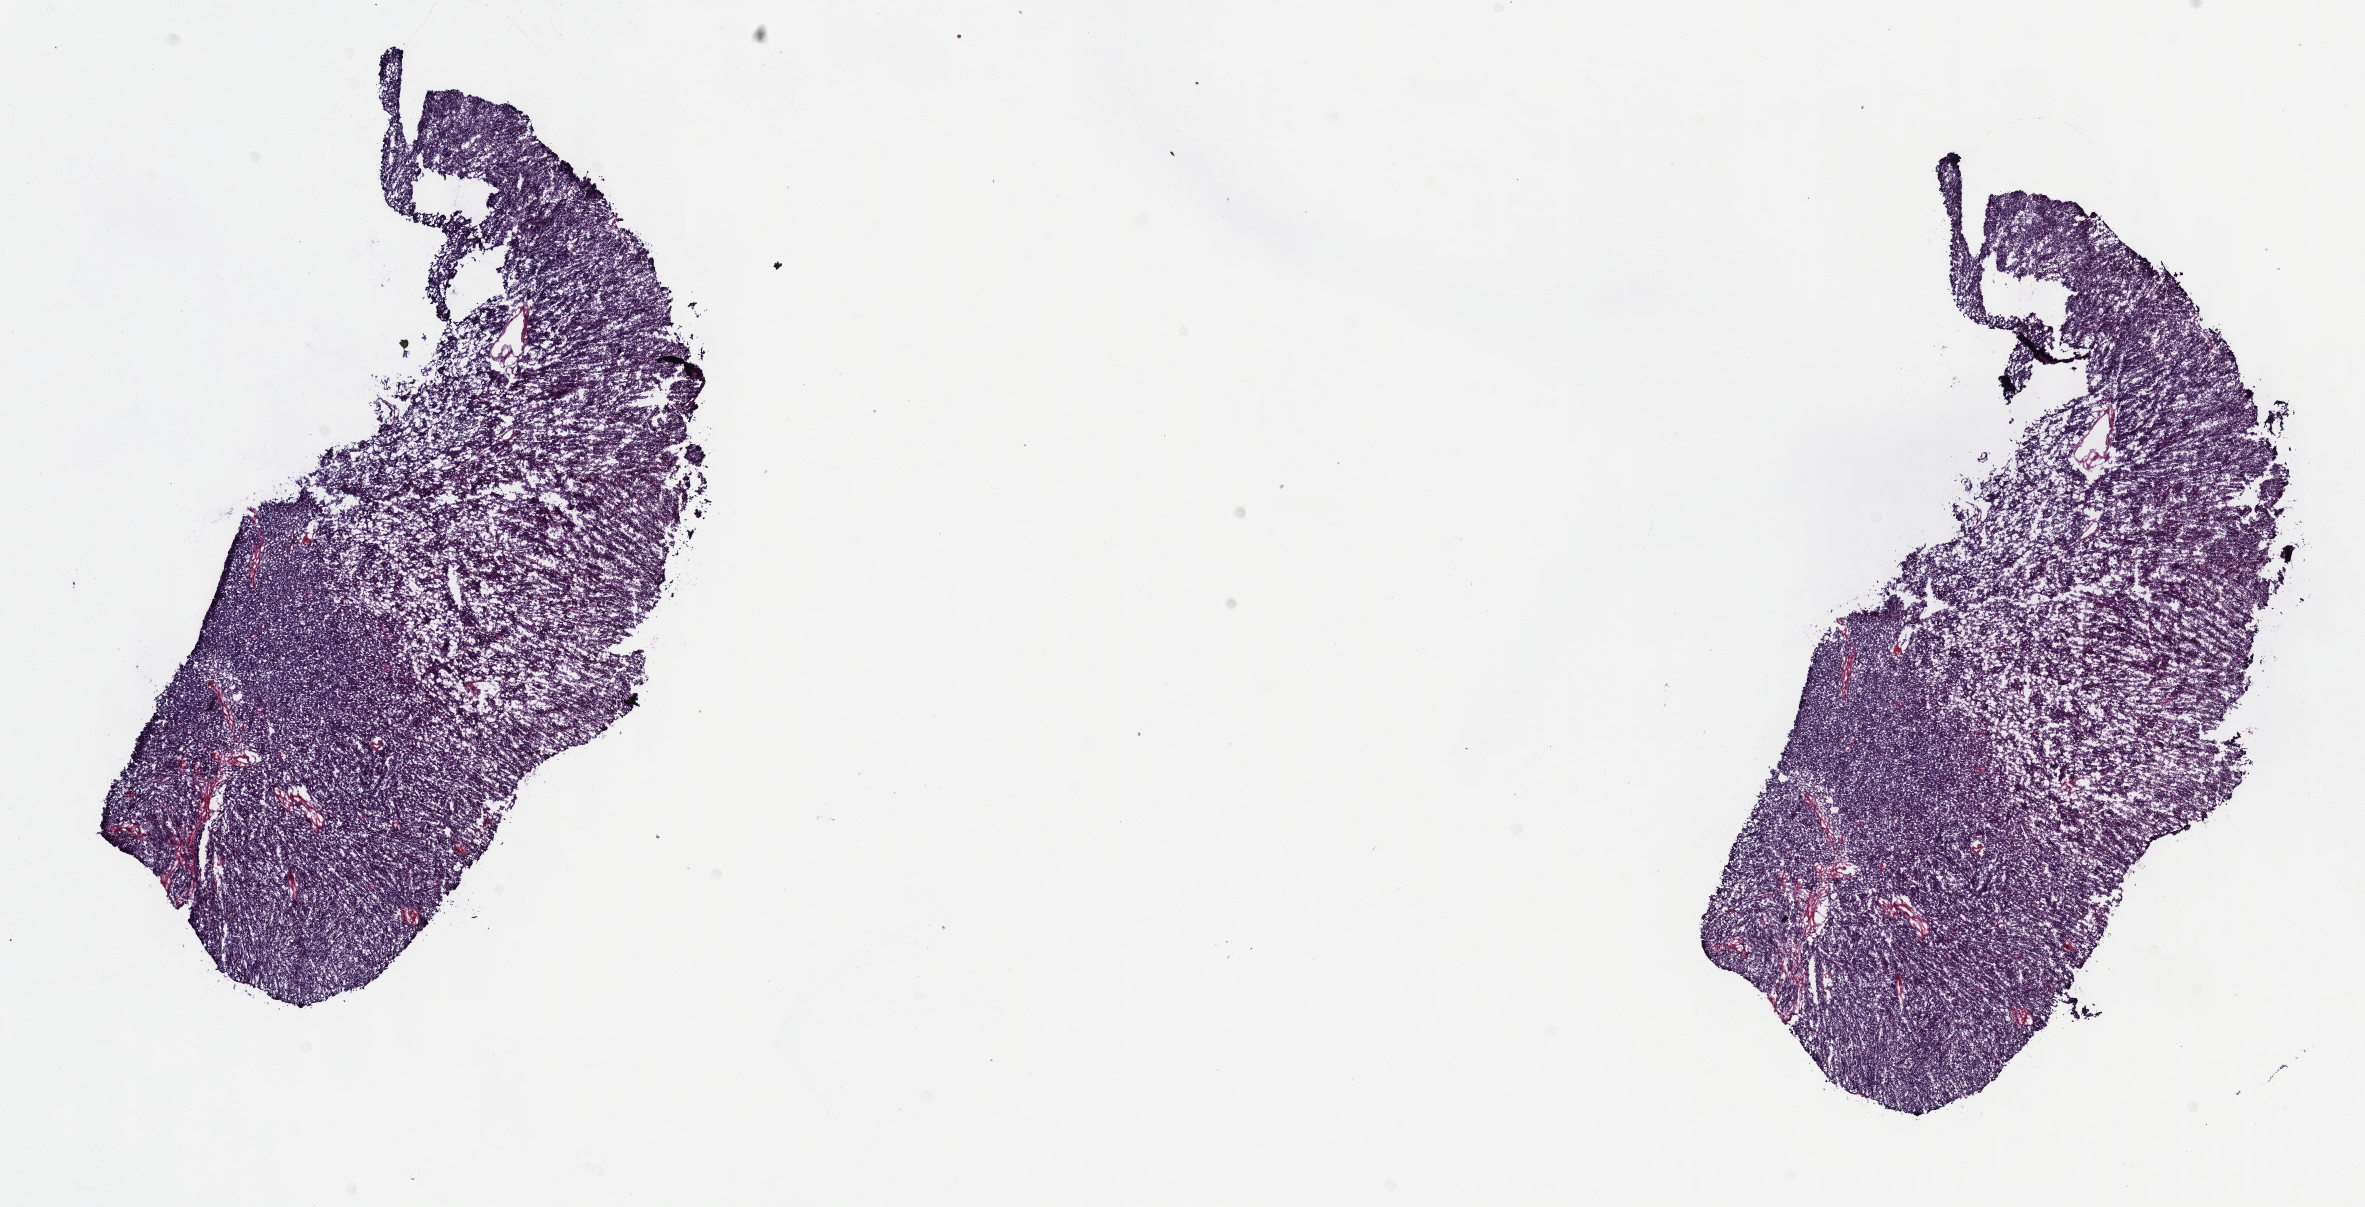
Digitized Hematoxylin and eosin (H&E) stained tissue section (whole slide), low-resolution overview of the scanned area, about 19.1 x 9.8 mm. Frozen section. Sample: primary tumour, thymus. Male, age 67 years at initial diagnosis. Composition of this section per pathologist review: tumour cells 90%, tumour nuclei 90%, normal cells 0%, stromal cells 10%, necrosis 0%. Inflammatory infiltration, as recorded: lymphocyte infiltration 0%, monocyte infiltration 0%, neutrophil infiltration 0%.
Pathologic diagnosis: Thymoma, type AB, NOS.